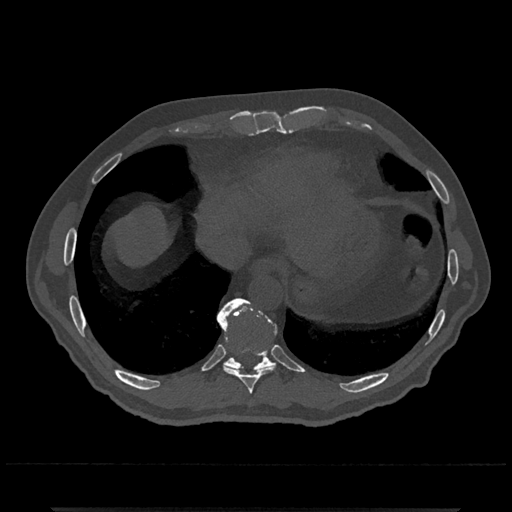
CT including the spine, one axial slice; position 589 of 797 along the scan axis; reconstruction kernel Br40s/3; 120 kVp; bone window (W 1800 / L 400 HU); 0.5 mm slice thickness; 512 × 512 image matrix. Patient: male, 67 years. Case-level facts recorded for this patient, not image findings: primary cancer: prostate.
Structures marked on this image (semi-automatic segmentation, software-assisted and operator-edited):
- T10 vertebra: bounding box (x1, y1, x2, y2) in pixels: (218, 298, 276, 372)
- T9 vertebra: (217, 308, 276, 394)